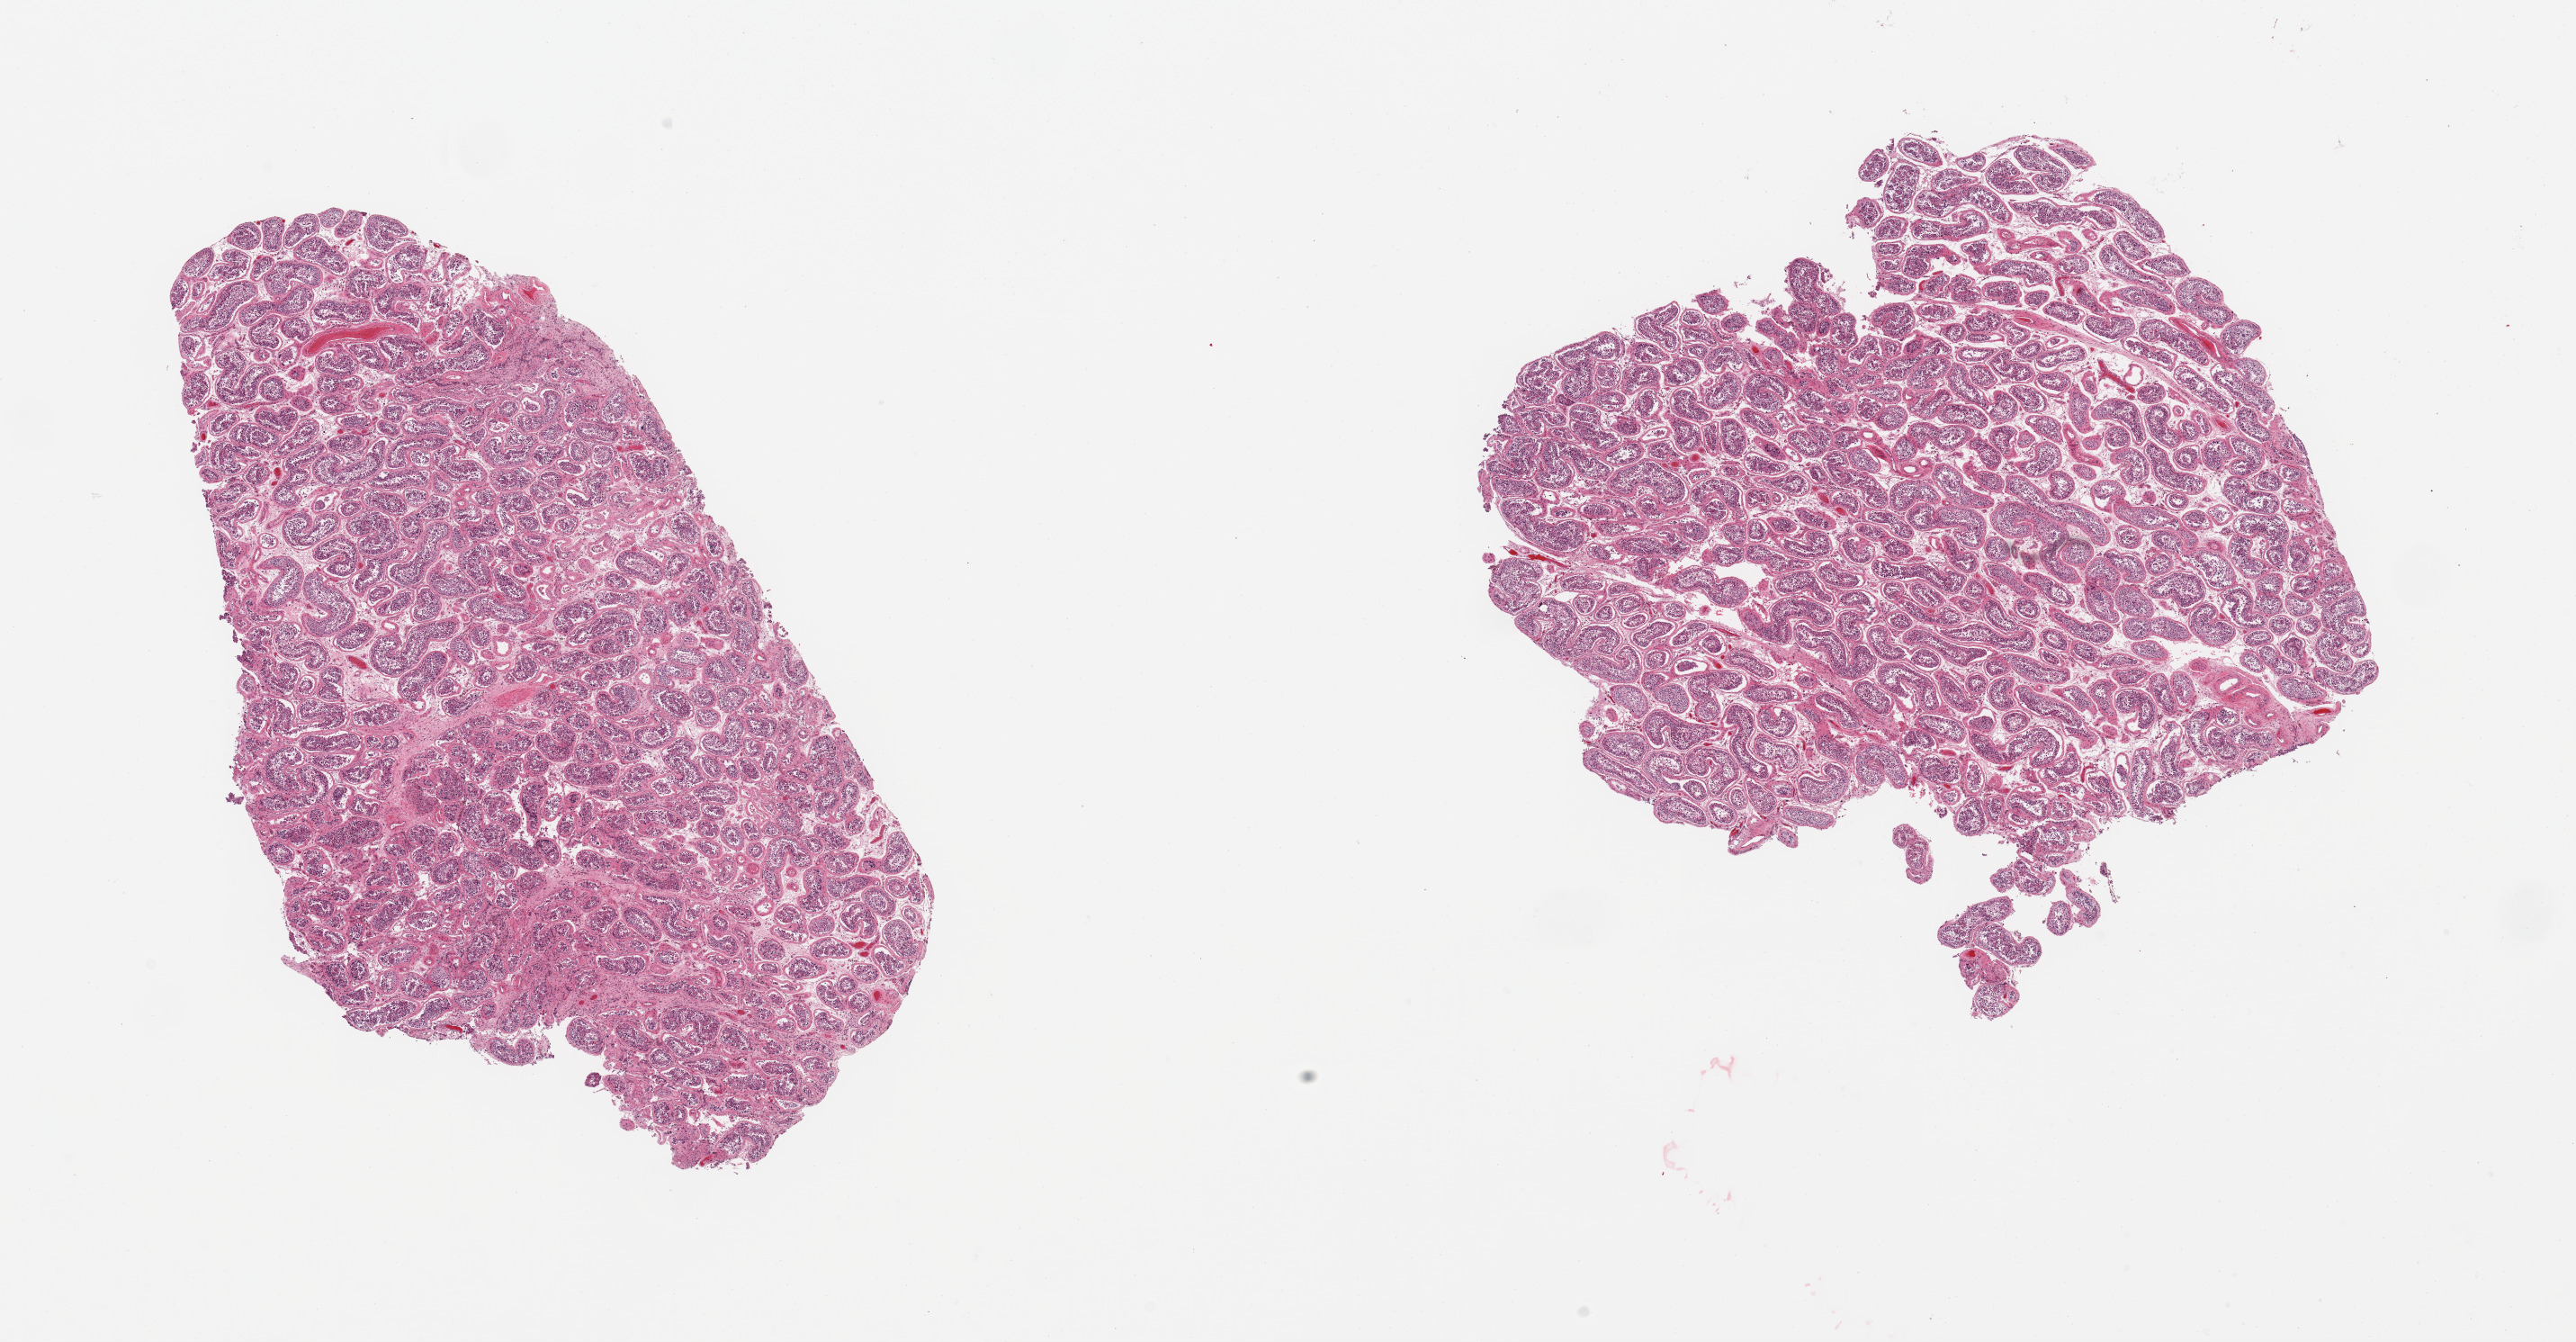
Whole-slide image, H&E stain — low-resolution overview of the scanned area, about 22.6 x 11.8 mm (from a 20x scan). PAXgene-fixed paraffin-embedded (PFPE) section. Section of testis (target tissue). Tissue donor sample. Donor: male.
Review note (as recorded): 2 pieces; spermatogenesis.